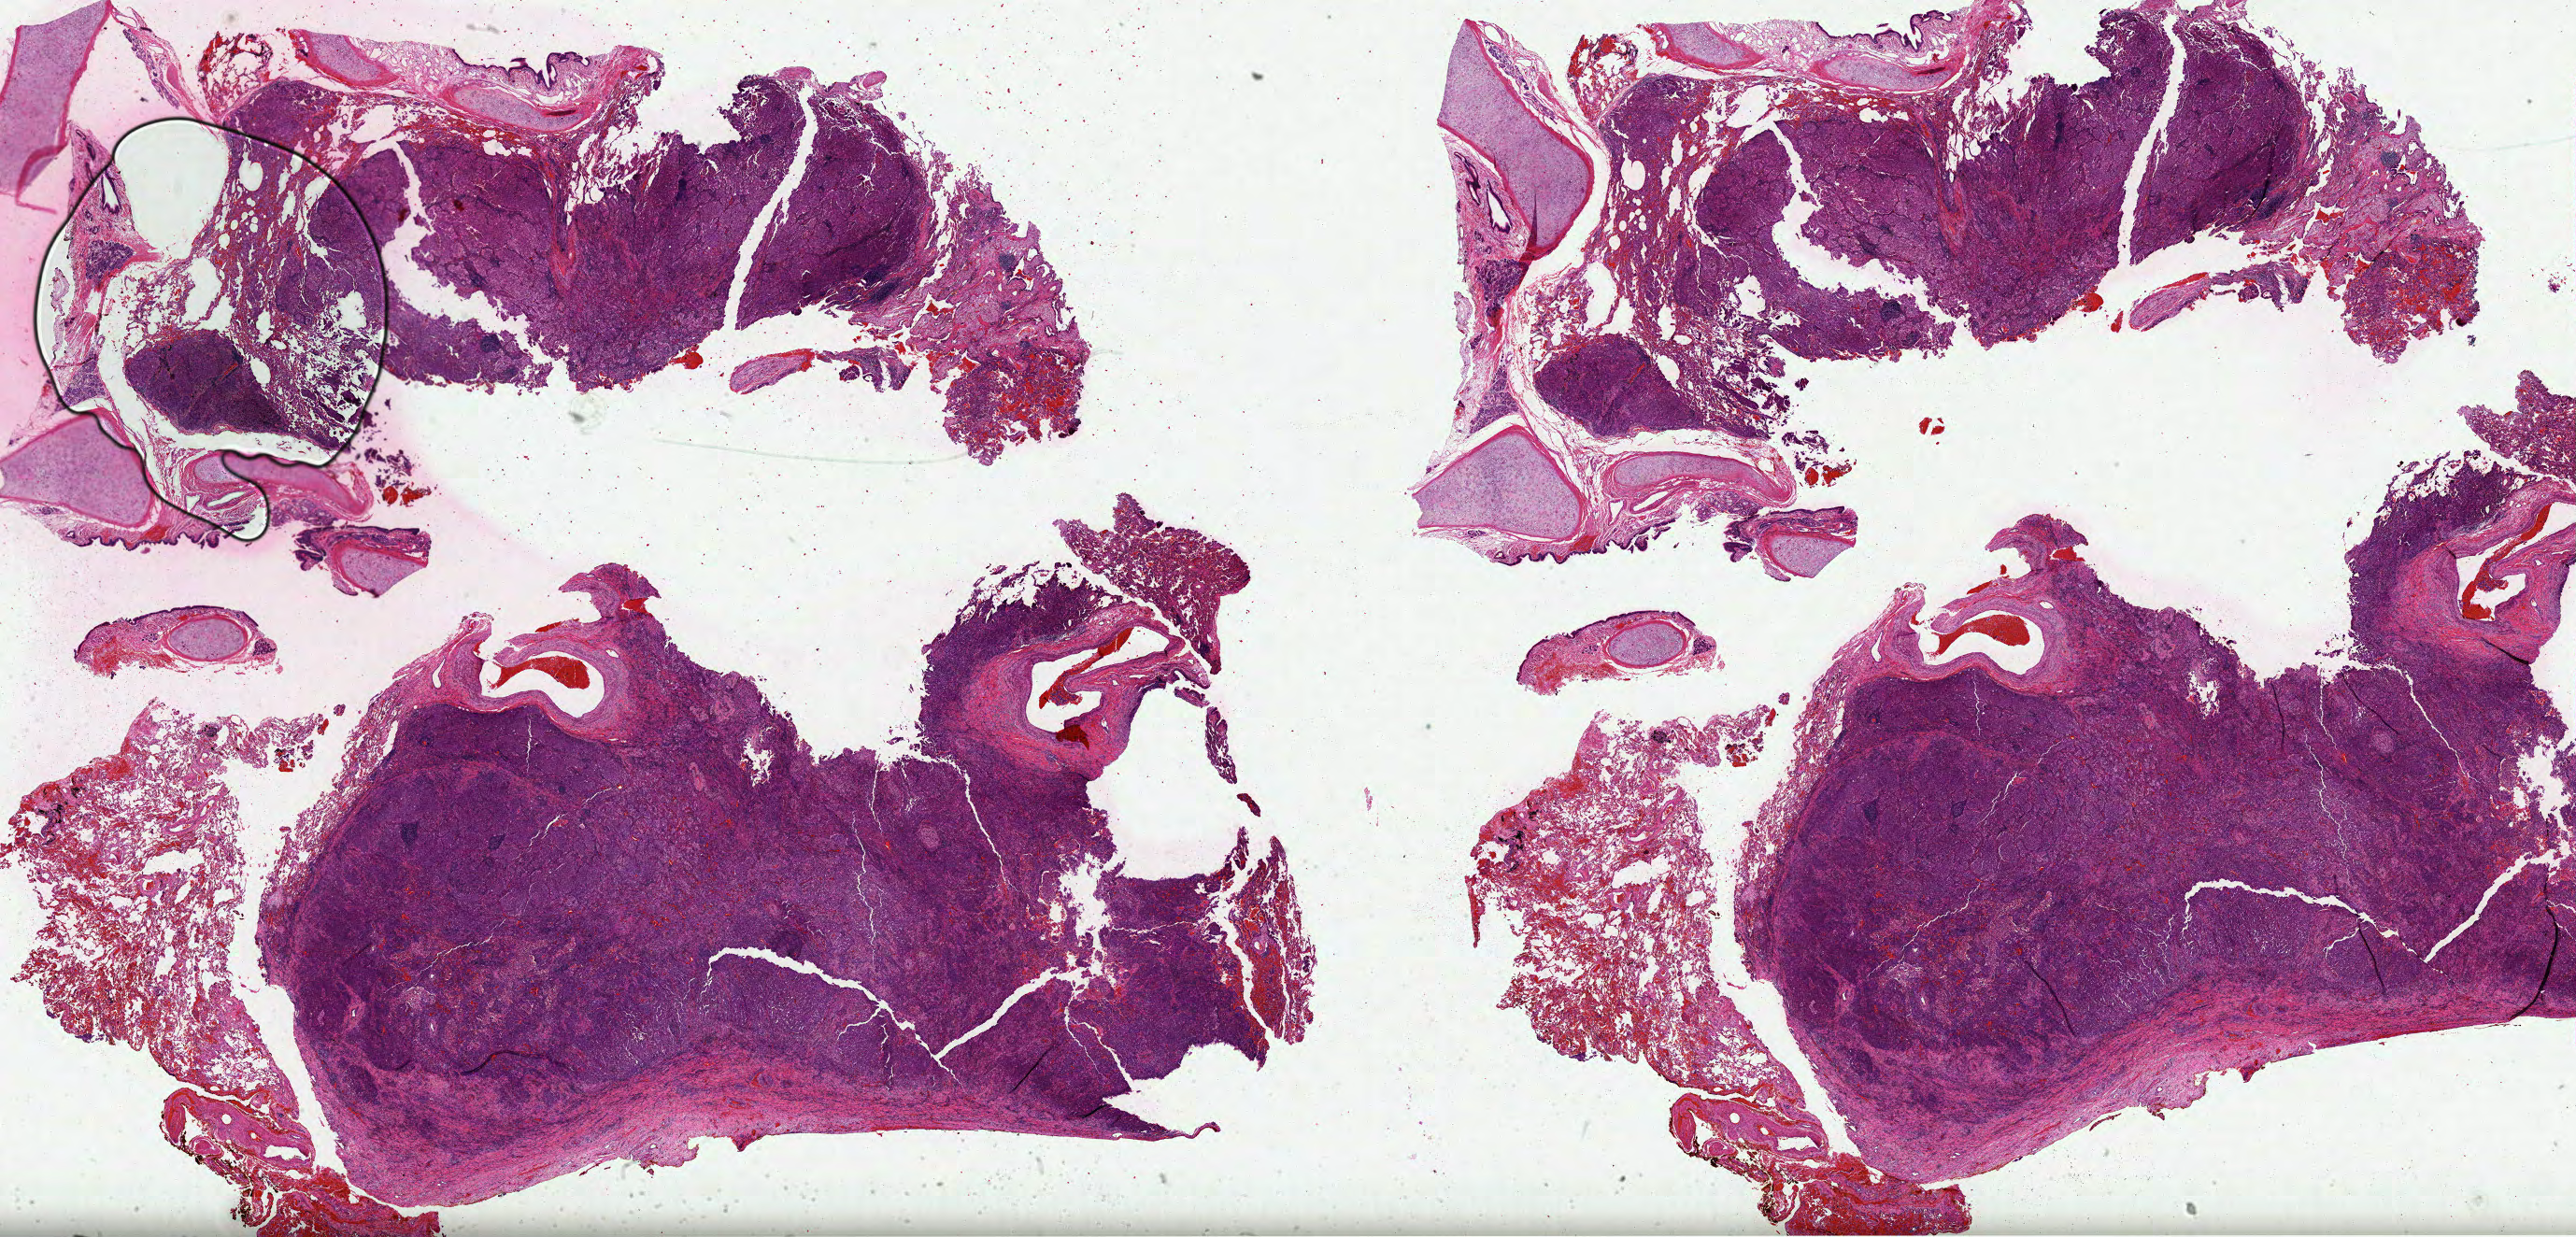
Digitized H&E-stained tissue section (whole slide) — shown as a low-resolution overview of the whole scanned area (about 44.5 x 21.4 mm), FFPE section, lung, primary tumour sample. Patient: male, age at initial diagnosis 82 years.
AJCC pathologic stage: IIIA. Histologic diagnosis: Papillary adenocarcinoma, NOS (upper lobe, lung).